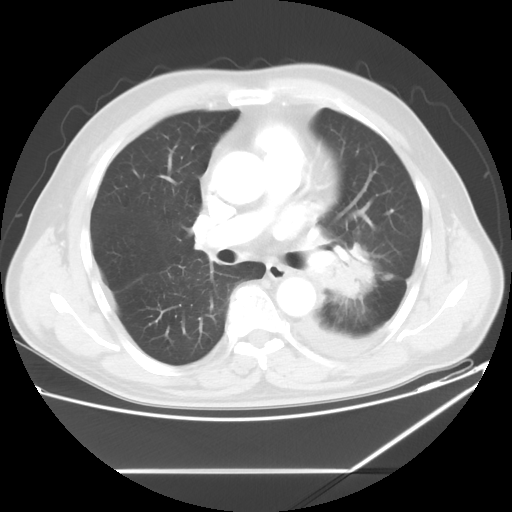
Chest CT, one axial slice. Position 33 of 60 along the scan axis. Lung window (W 1500 / L -600 HU). 5 mm slice thickness. 512 × 512 image matrix, field of view 395 × 395 mm. Patient: male, 62 years. Case-level facts recorded for this patient, not image findings: clinical TNM (as recorded): T3 N0 M1.
Structures marked on this image (bounding box drawn by a radiologist):
- lung tumour (recorded histology: adenocarcinoma): bounding box <319,242,378,299> (left, top, right, bottom; pixels)
- lung tumour (recorded histology: adenocarcinoma): <327,248,374,302>